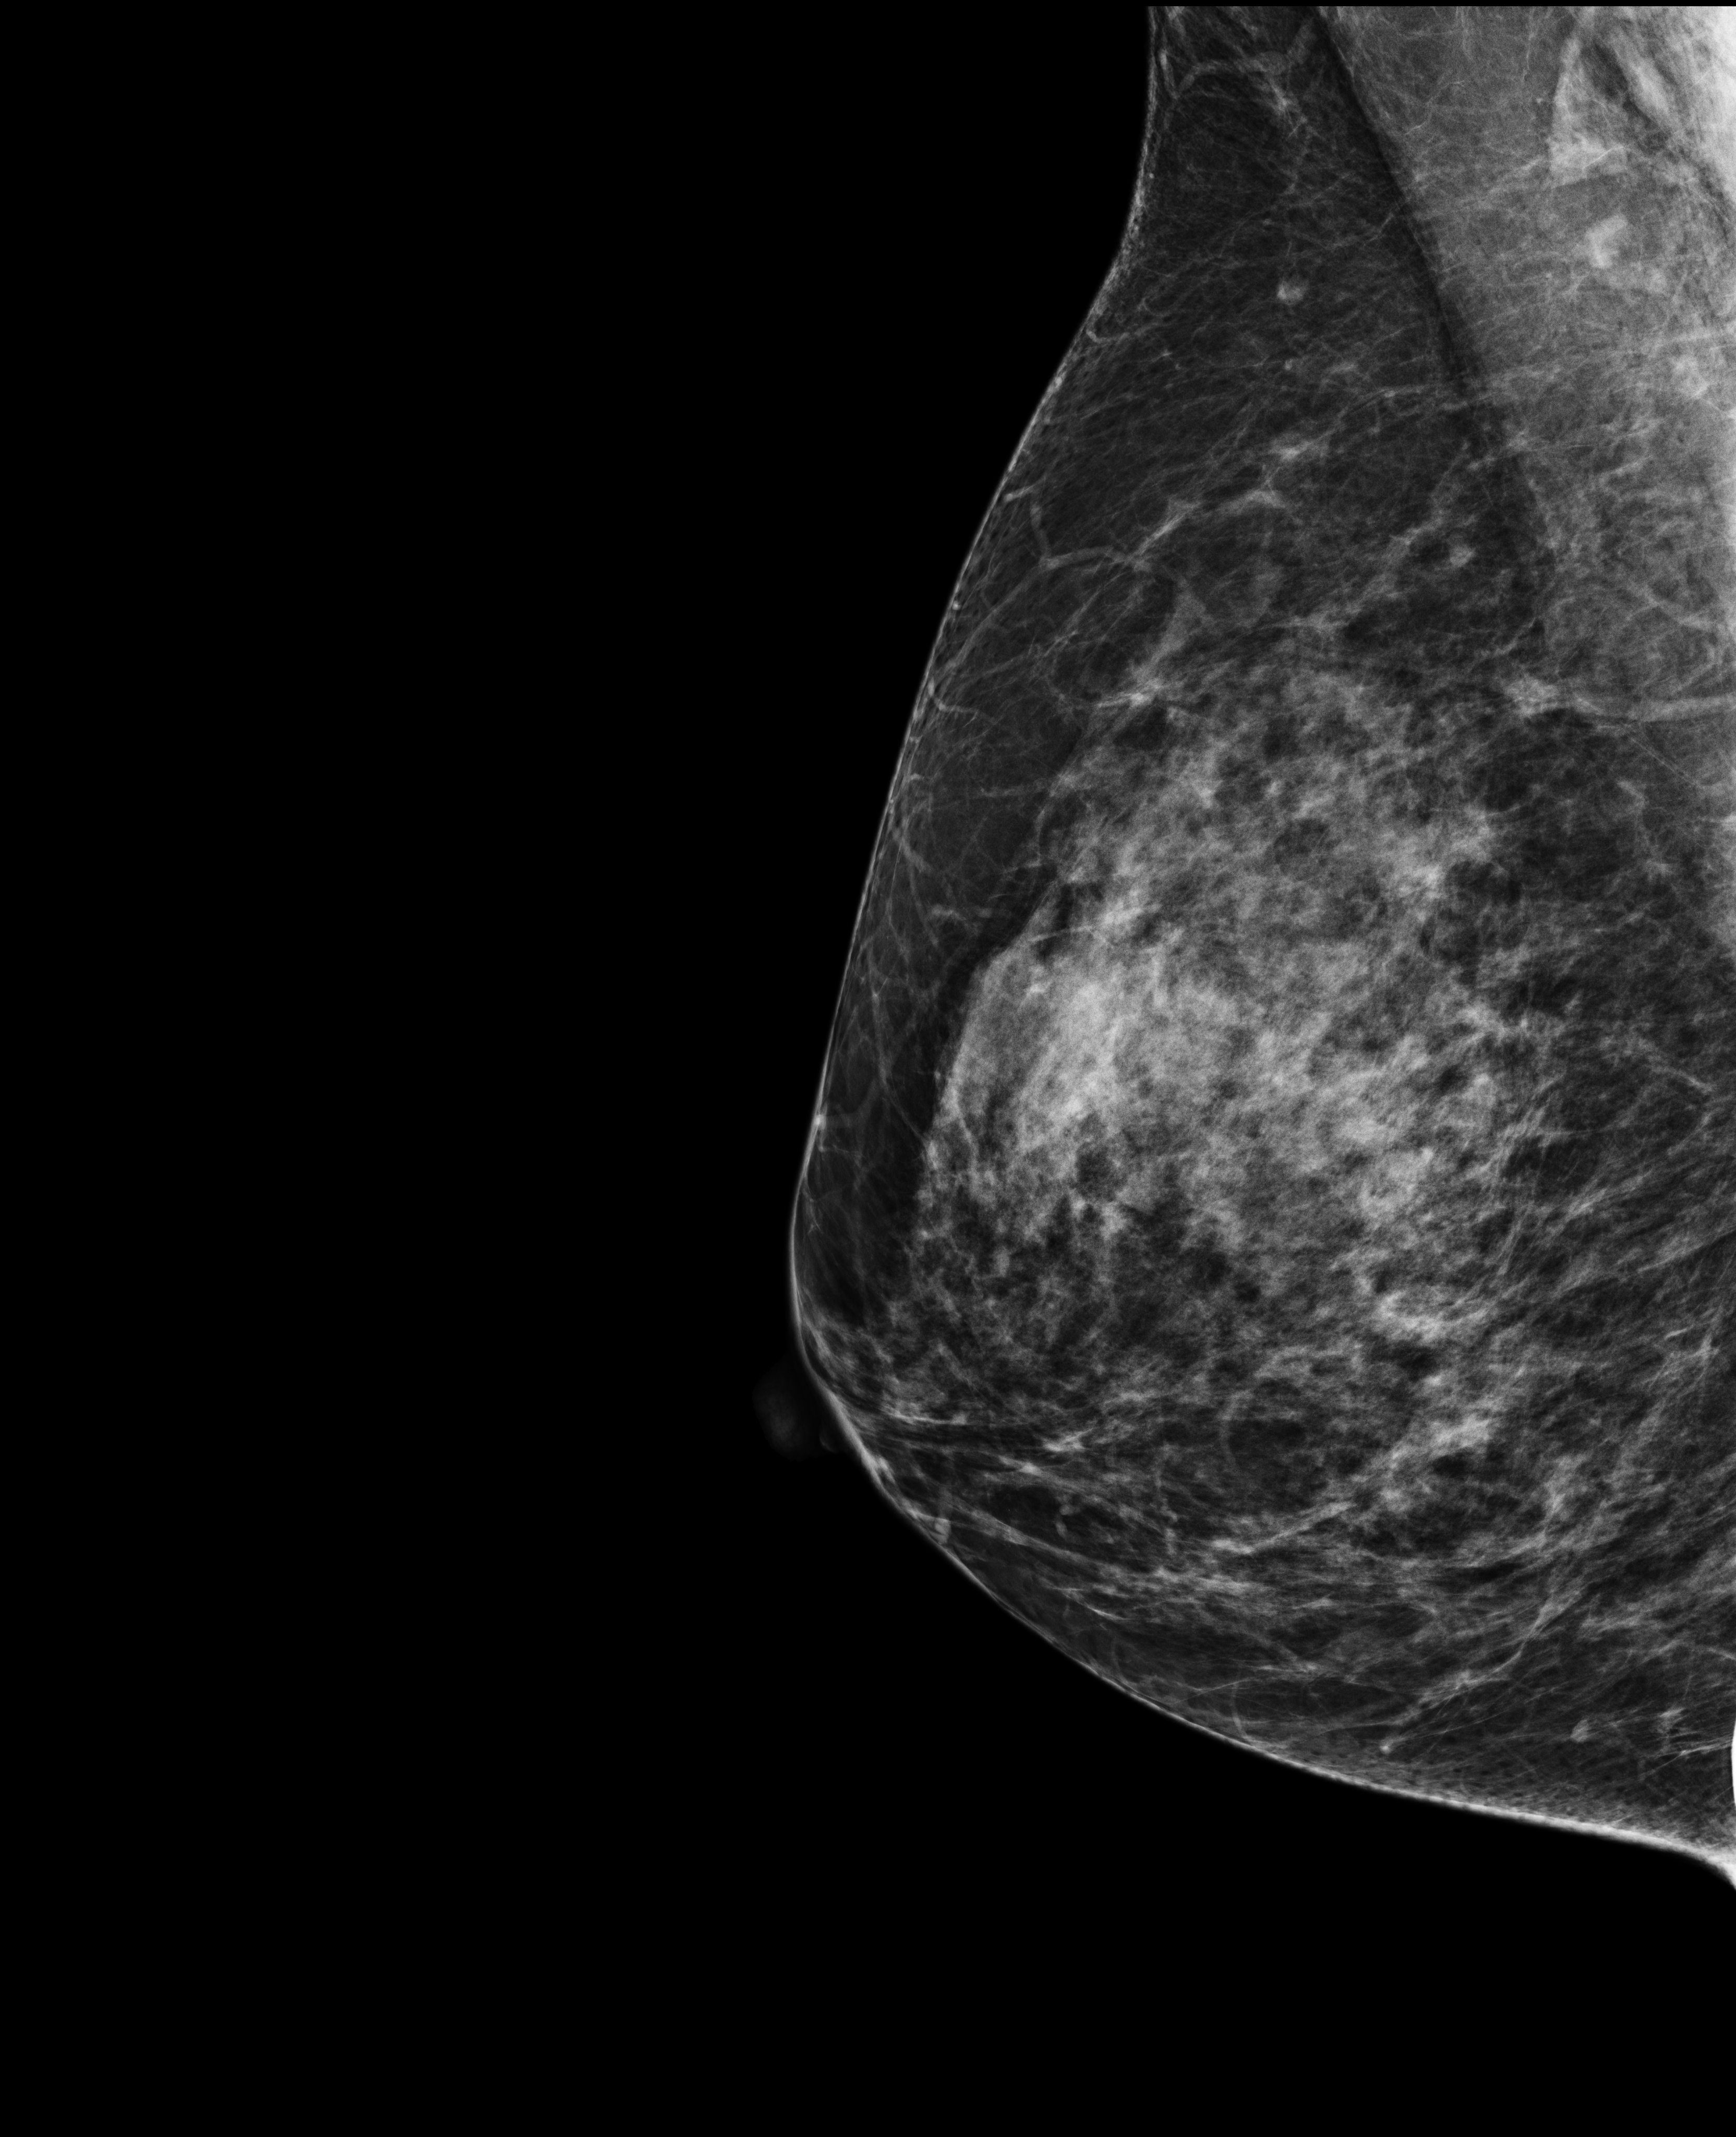
Annual screening mammography examination, compressed breast thickness 75 mm, system: Selenia Dimensions. Female patient, age 47 years.
Image type: full-field digital mammogram. Breast: right. Projection: MLO view.